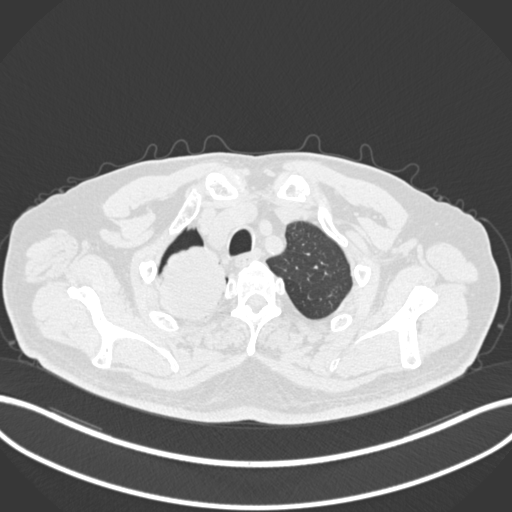
Chest CT, one axial slice; reconstruction kernel B30f; 120 kVp; lung window (W 1500 / L -600 HU); 1 mm slice thickness; 512 × 512 image matrix, field of view 400 × 400 mm. Patient: male, 68 years. Case-level facts recorded for this patient, not image findings: clinical TNM (as recorded): T2a N0 M0.
Outlined on this slice (rectangle marked by the reading radiologist):
- lung tumour (recorded histology: adenocarcinoma): bounding box [x1, y1, x2, y2] px = [155, 245, 229, 321]